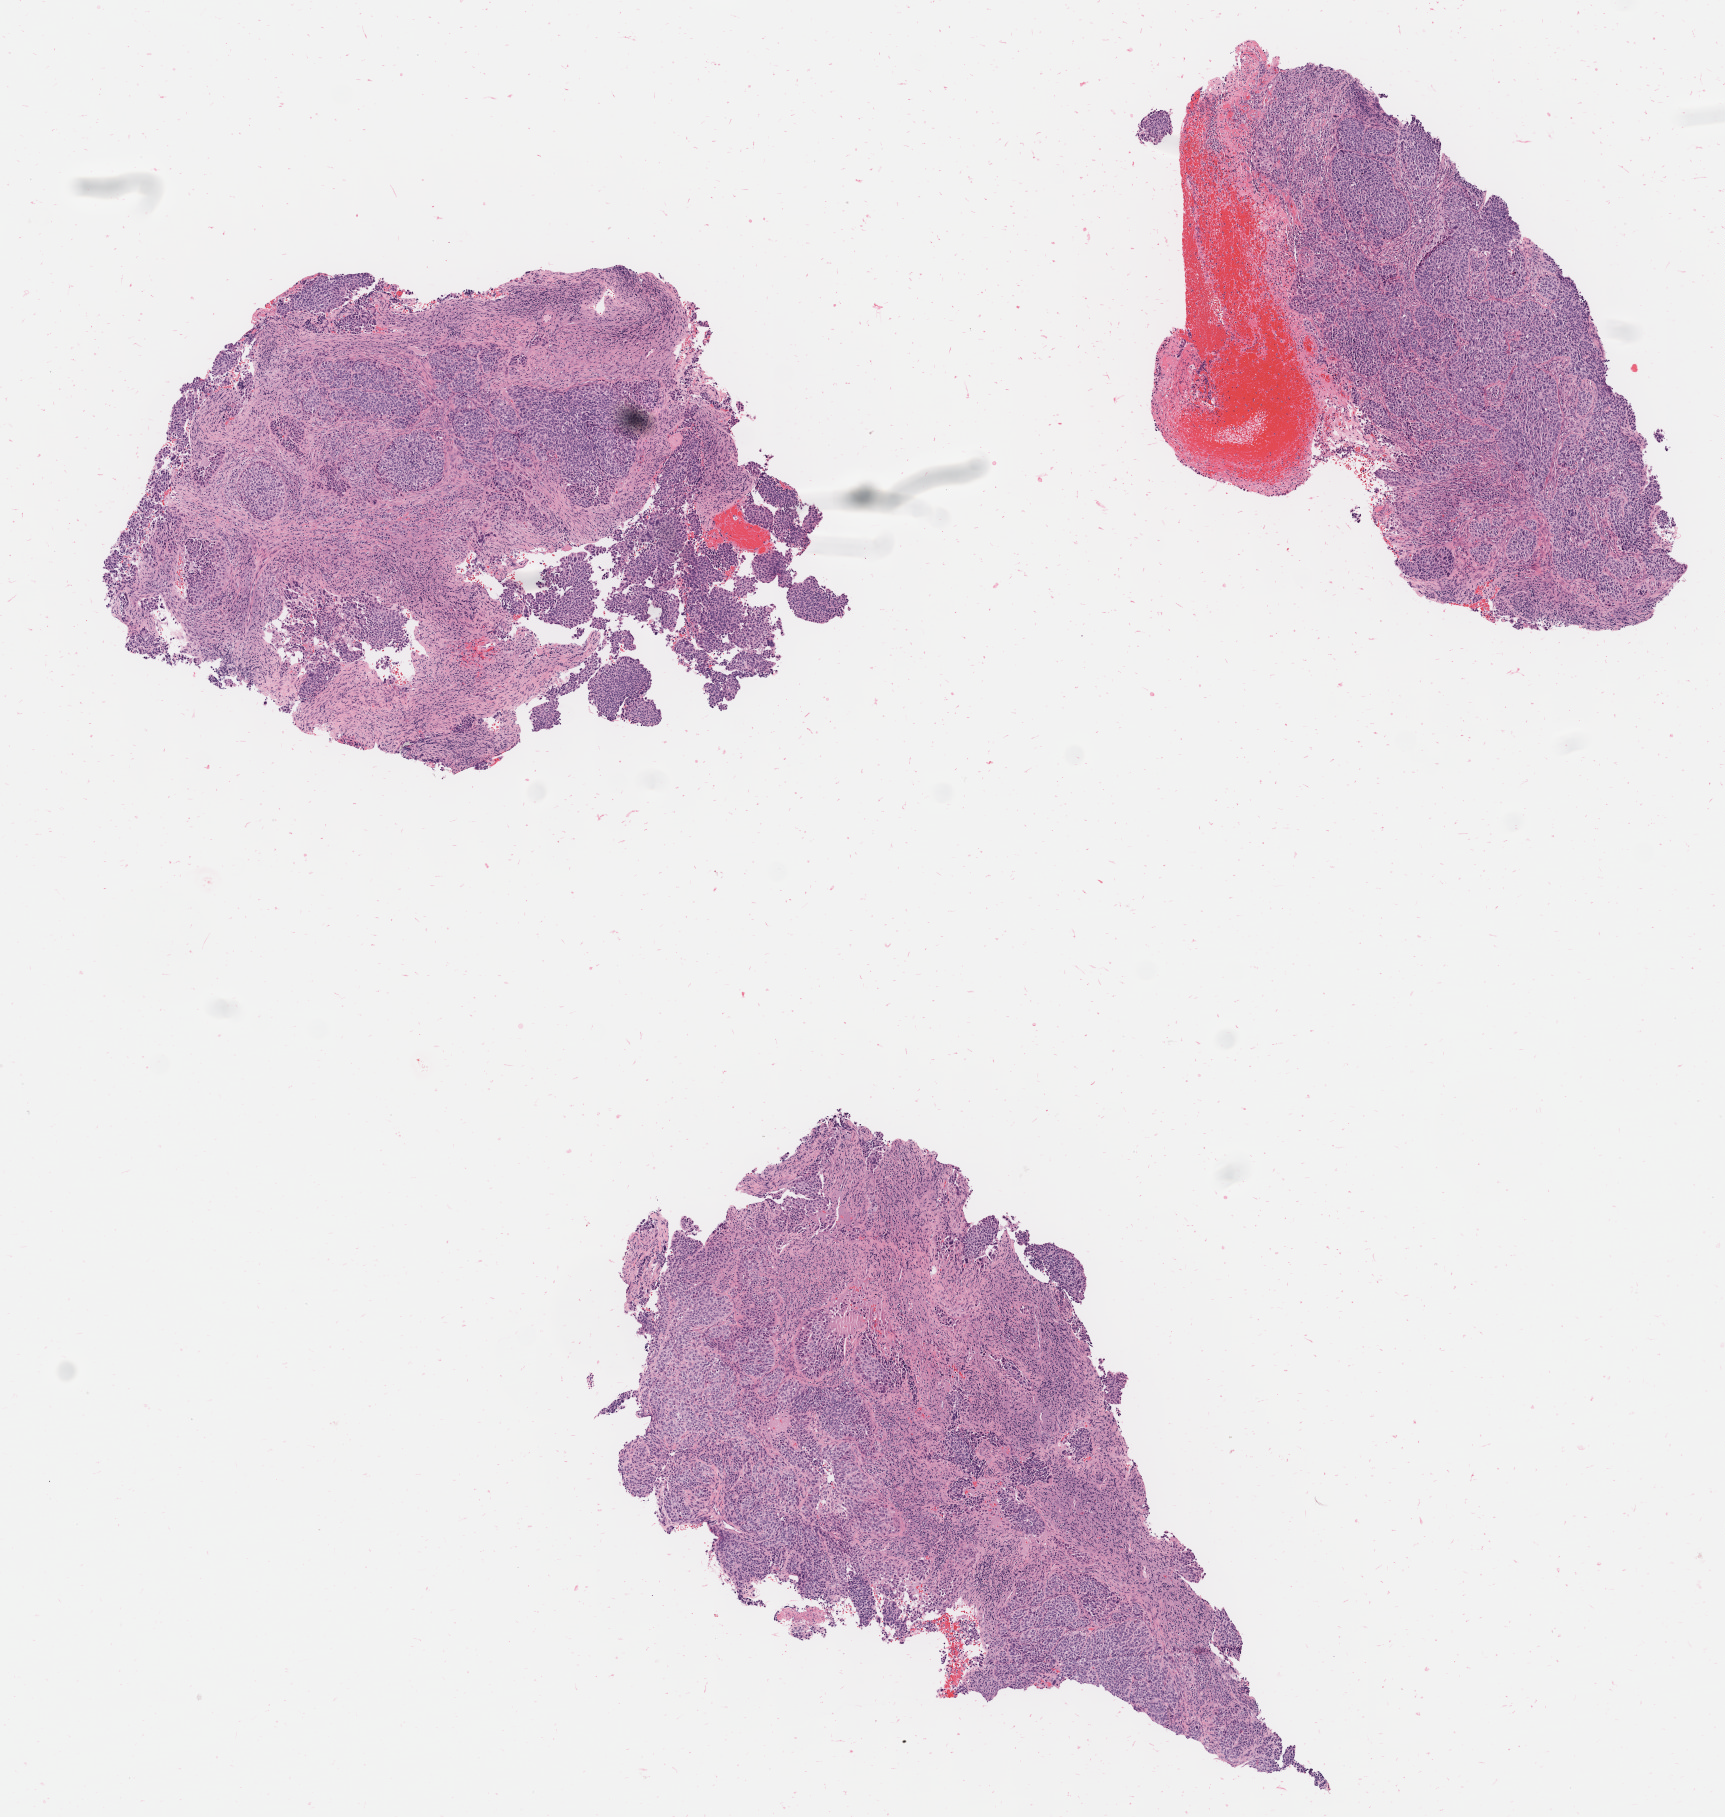
Haematoxylin and eosin whole-slide image — whole scanned area (about 6.9 x 7.2 mm) shown as a low-resolution overview, specimen: tumor tissue, site: cervix. Patient: female, age 34 years.
Histologic diagnosis: Squamous cell carcinoma, large cell, nonkeratinizing, NOS.